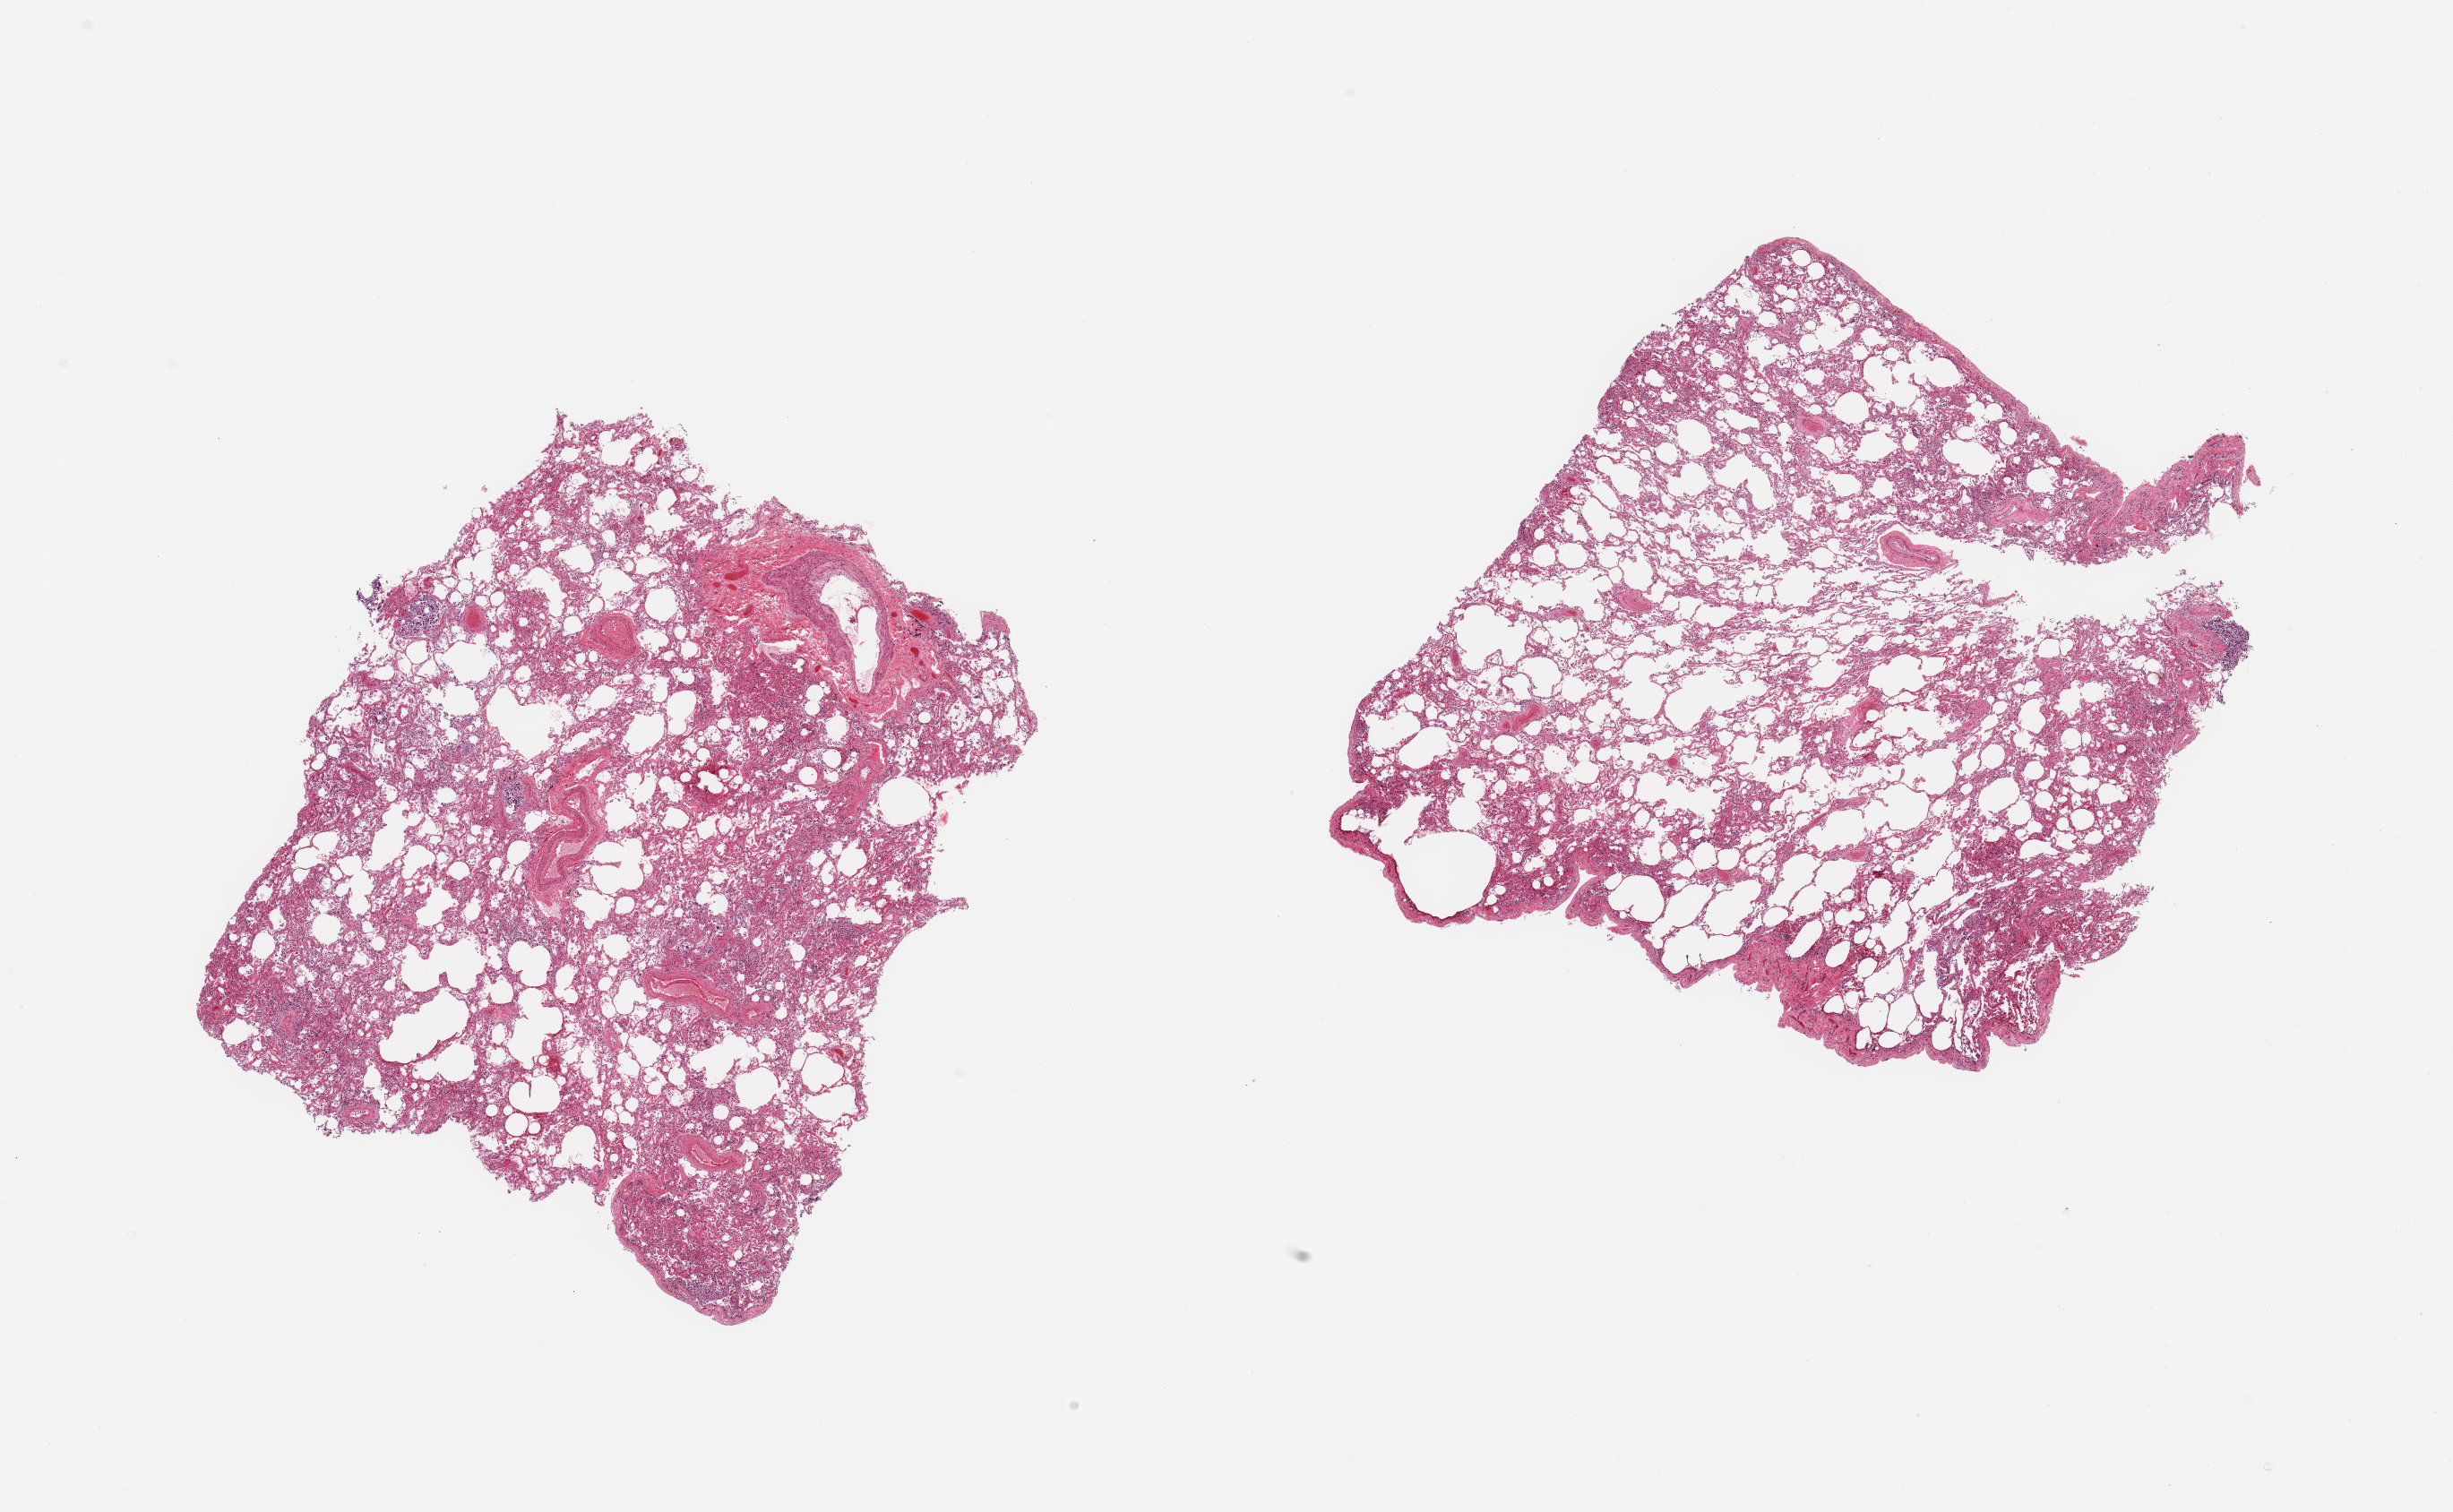
Whole-slide image, H&E stain — a low-resolution overview of the entire scanned area, about 21.7 x 13.4 mm, PAXgene-fixed, paraffin-embedded tissue, sampled site (target tissue): lung, tissue donor sample.
Review note (as recorded): 2 pieces; patchy pneumonia, some widened airspaces.